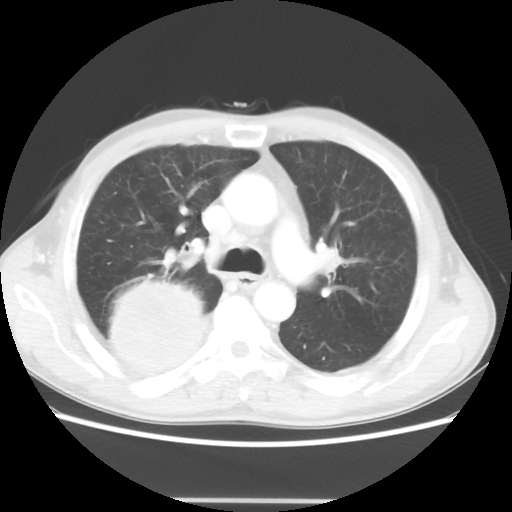
Chest CT, one axial slice. Slice 32 of 48 in the series (ordered by position). Reconstruction kernel STANDARD. Lung window (W 1500 / L -600 HU). 5 mm slice thickness. 512 × 512 image matrix, field of view 361 × 361 mm. Male patient, age 66 years. Case-level facts recorded for this patient, not image findings: clinical TNM (as recorded): T4 N1 M1; histopathological grade: G3.
Annotated regions visible in this slice (bounding box drawn by a radiologist):
- lung tumour (recorded histology: small cell carcinoma): bounding box [x1, y1, x2, y2] px = [100, 276, 207, 371]